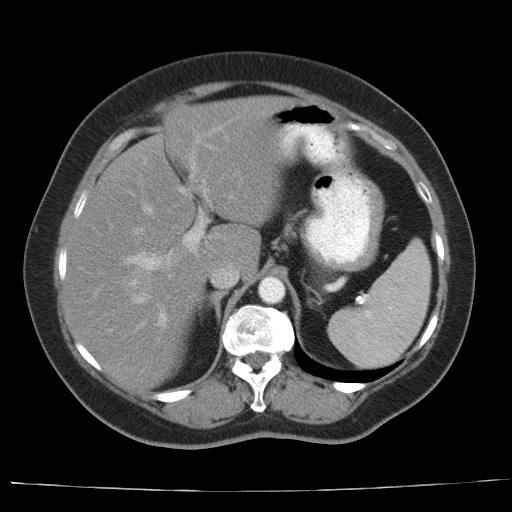
Contrast-enhanced abdominal CT, one axial slice; position 23 of 44 along the scan axis; 140 kVp; intravenous contrast given; soft-tissue window (W 400 / L 40 HU); 5 mm slice thickness; 512 × 512 image matrix. Female patient. From the clinical record (not read from this slice): diagnosis: colorectal cancer liver metastases, imaged before liver resection.
Annotated regions visible in this slice (expert manual segmentation):
- hepatic veins: bounding box (x1, y1, x2, y2) in pixels: (134, 206, 152, 327)
- liver: (60, 96, 293, 390)
- planned liver remnant (the part of the liver to remain after resection): (101, 96, 292, 278)
- portal vein (with intrahepatic branches): (109, 116, 238, 331)